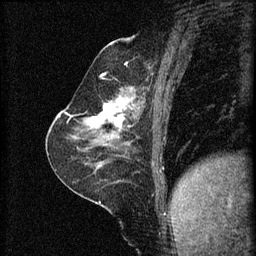
Breast MRI (dynamic contrast-enhanced), one sagittal slice. Position 28 of 60 along the scan axis. 3 images stored at this slice position (order not interpretable as contrast timing). 1.5 T. TE 4.2 ms, TR 8.2 ms. 256 × 256 image matrix, field of view 180 × 180 mm. Patient: female, 59 years.
Annotated regions visible in this slice (semi-automatically segmented with operator editing):
- analysis volume of interest (the breast-tissue region the enhancement analysis was run in; not a lesion): bounding box <78,92,137,135> (left, top, right, bottom; pixels)
- tumour enhancement mask (voxels above the 70 % enhancement threshold inside the analysis volume of interest): <90,96,127,129>